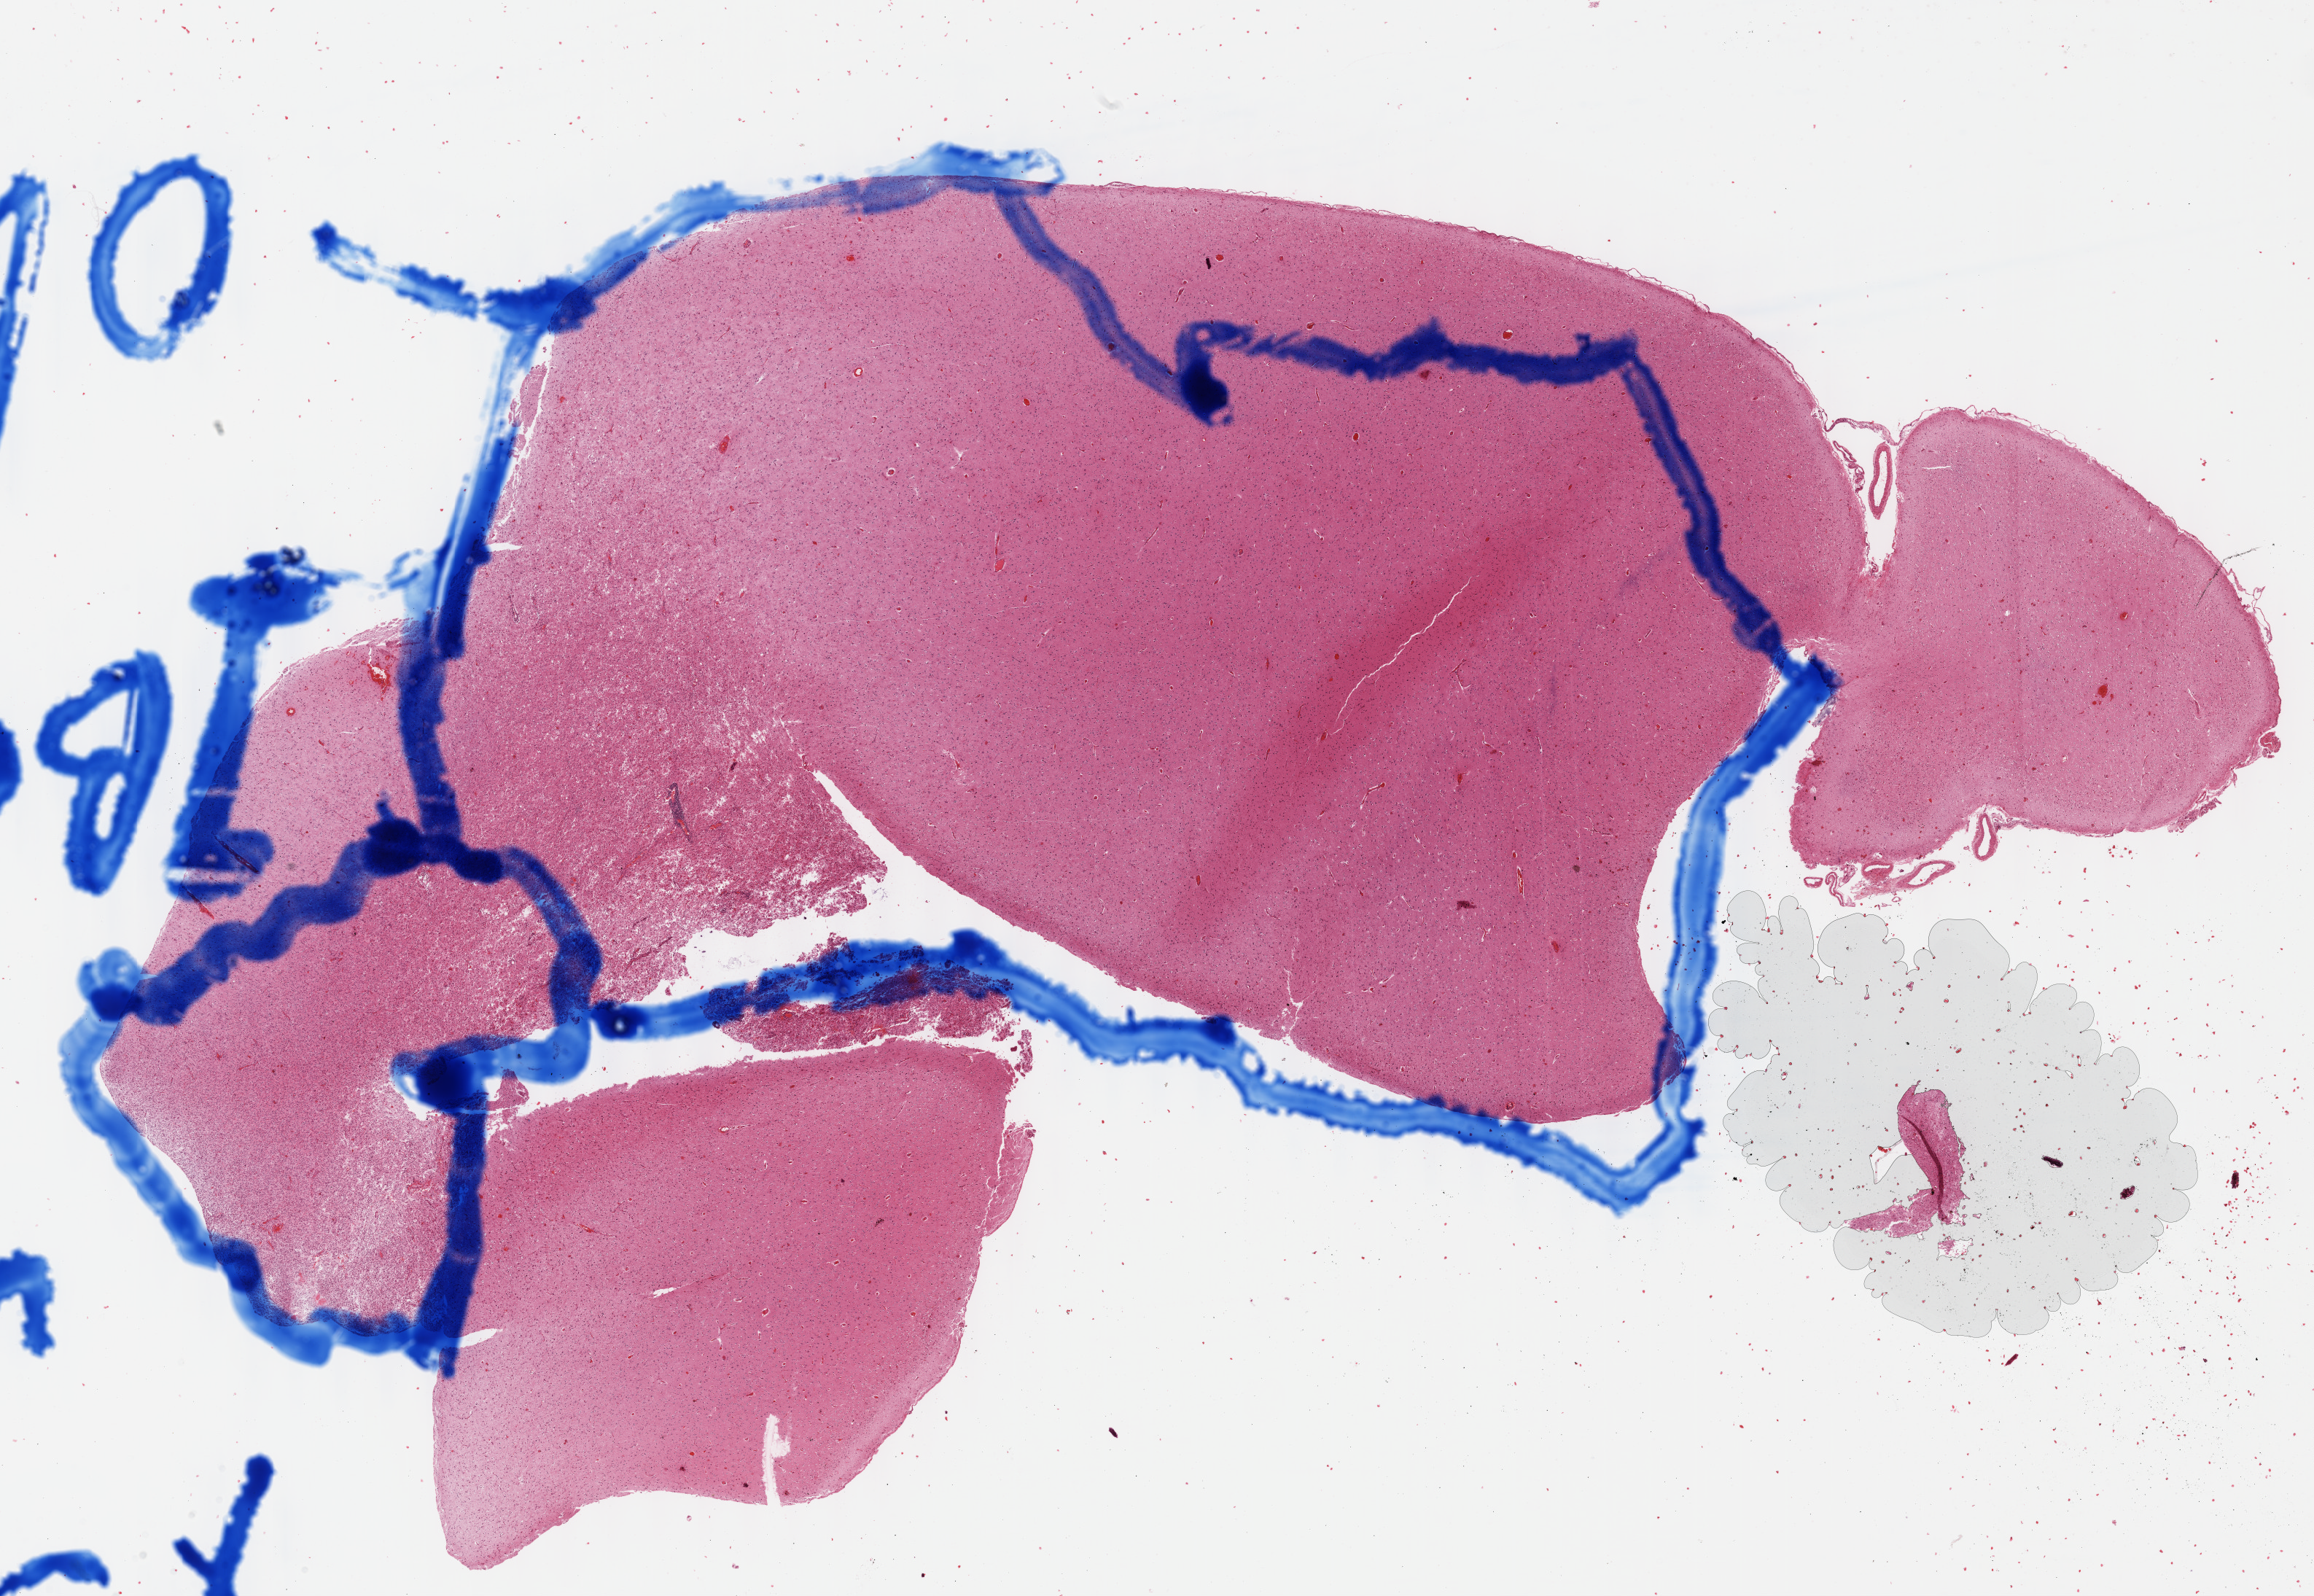
Whole-slide histology image, H&E, a low-resolution overview of the entire scanned area, about 25.7 x 17.7 mm. FFPE section. Sample: primary tumour, brain. Male, age 50 years at initial diagnosis.
• pathologic diagnosis: Glioblastoma